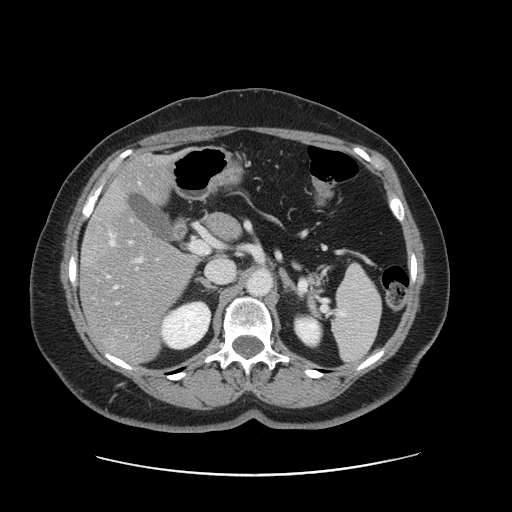
Contrast-enhanced abdominal CT, one axial slice; slice 81 of 161 in the series (ordered by position); 120 kVp; soft-tissue window (W 400 / L 40 HU); 512 × 512 image matrix, field of view 398 × 398 mm. Female patient, age 62 years. Case-level facts recorded for this patient, not image findings: diagnosis: colorectal cancer liver metastases, imaged before liver resection.
Outlined on this slice (expert manual segmentation):
- hepatic veins: bounding box [x1, y1, x2, y2] px = [108, 182, 141, 289]
- liver: [81, 156, 237, 362]
- planned liver remnant (the part of the liver to remain after resection): [113, 157, 238, 239]
- portal vein (with intrahepatic branches): [128, 241, 142, 262]